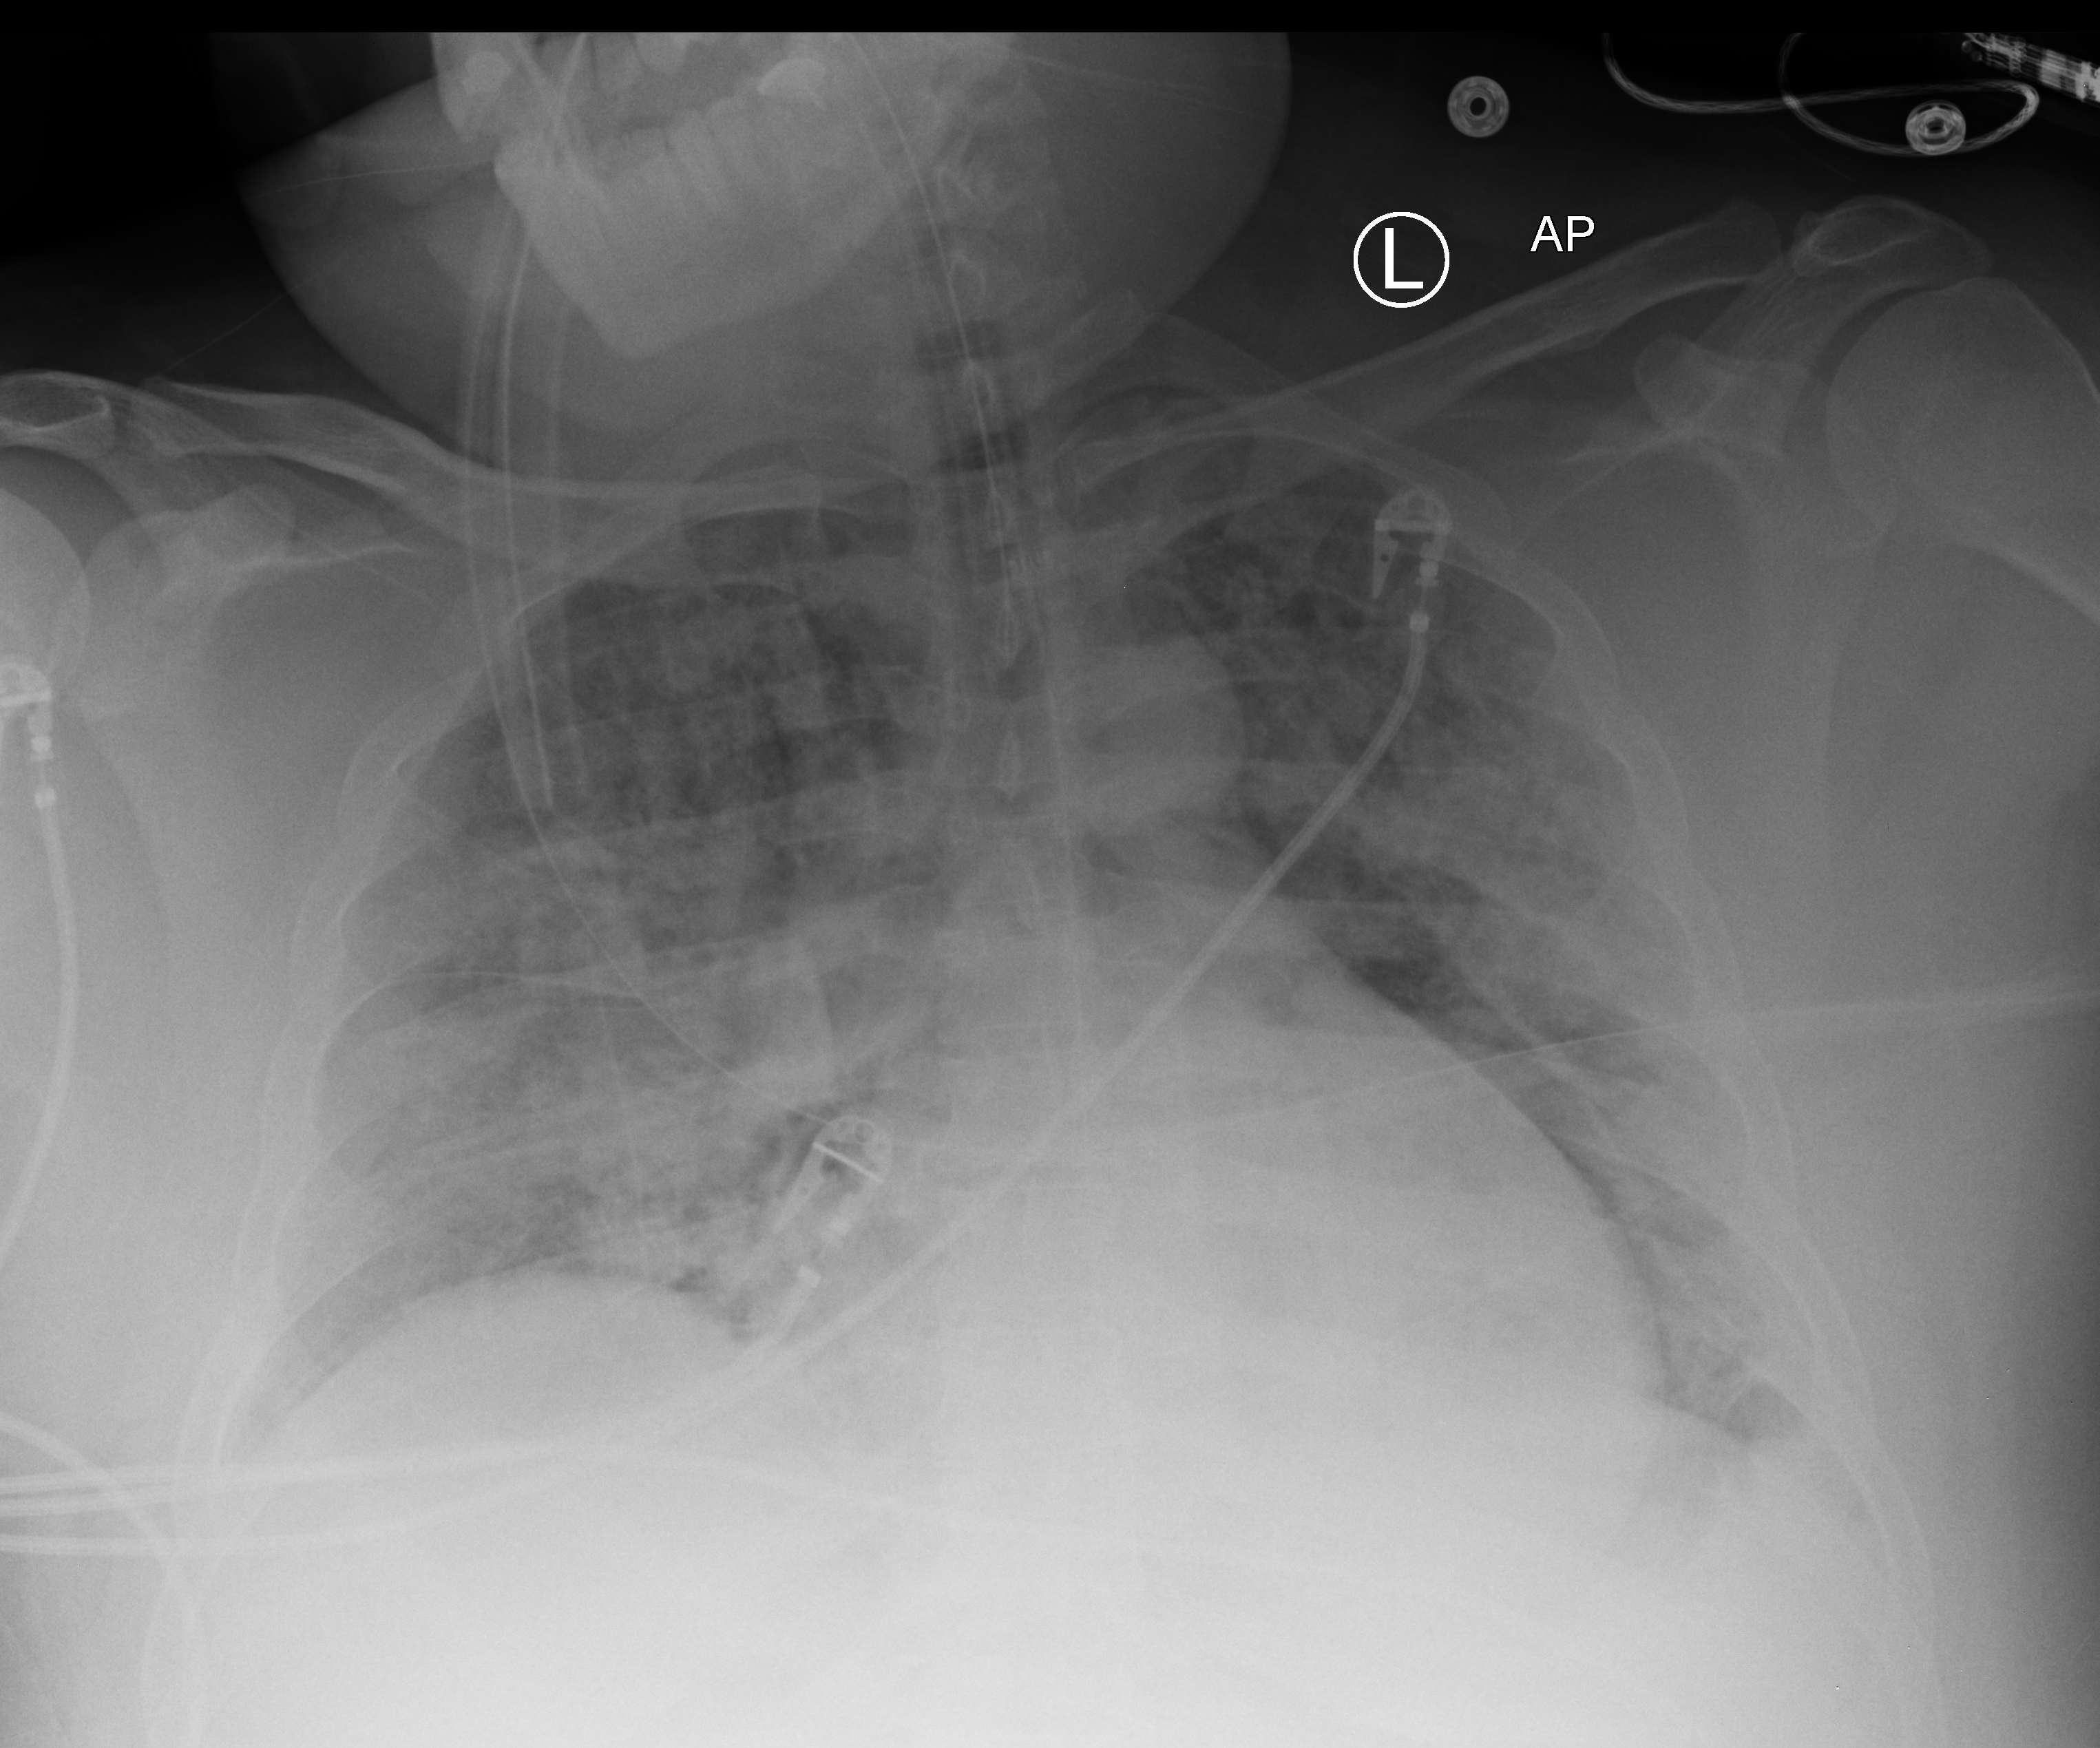
Bedside chest radiograph (computed radiography), anteroposterior (AP) projection. Adult patient hospitalised with COVID-19, age 18–59 years.
From the hospital-stay record, not from the radiograph (when in the stay this image was taken is not recorded): diabetes (admission record): no; mechanically ventilated during this hospital stay: yes.